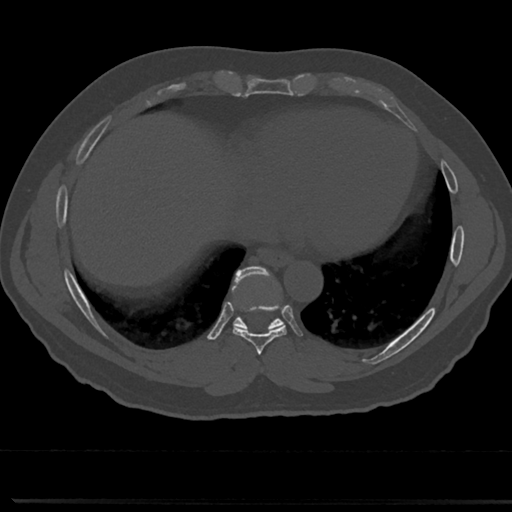
CT including the spine, one axial slice. Position 338 of 817 along the scan axis. Reconstruction kernel Br40s/3. Bone window (W 1800 / L 400 HU). 0.5 mm slice thickness. 512 × 512 image matrix, field of view 355 × 355 mm. Patient: male, 61 years. From the clinical record (not read from this slice): primary cancer: prostate.
Outlined on this slice (semi-automatic segmentation, software-assisted and operator-edited):
- T7 vertebra: box from (x=258, y=344) to (x=266, y=377) px
- T8 vertebra: (x=213, y=271)–(x=308, y=355)